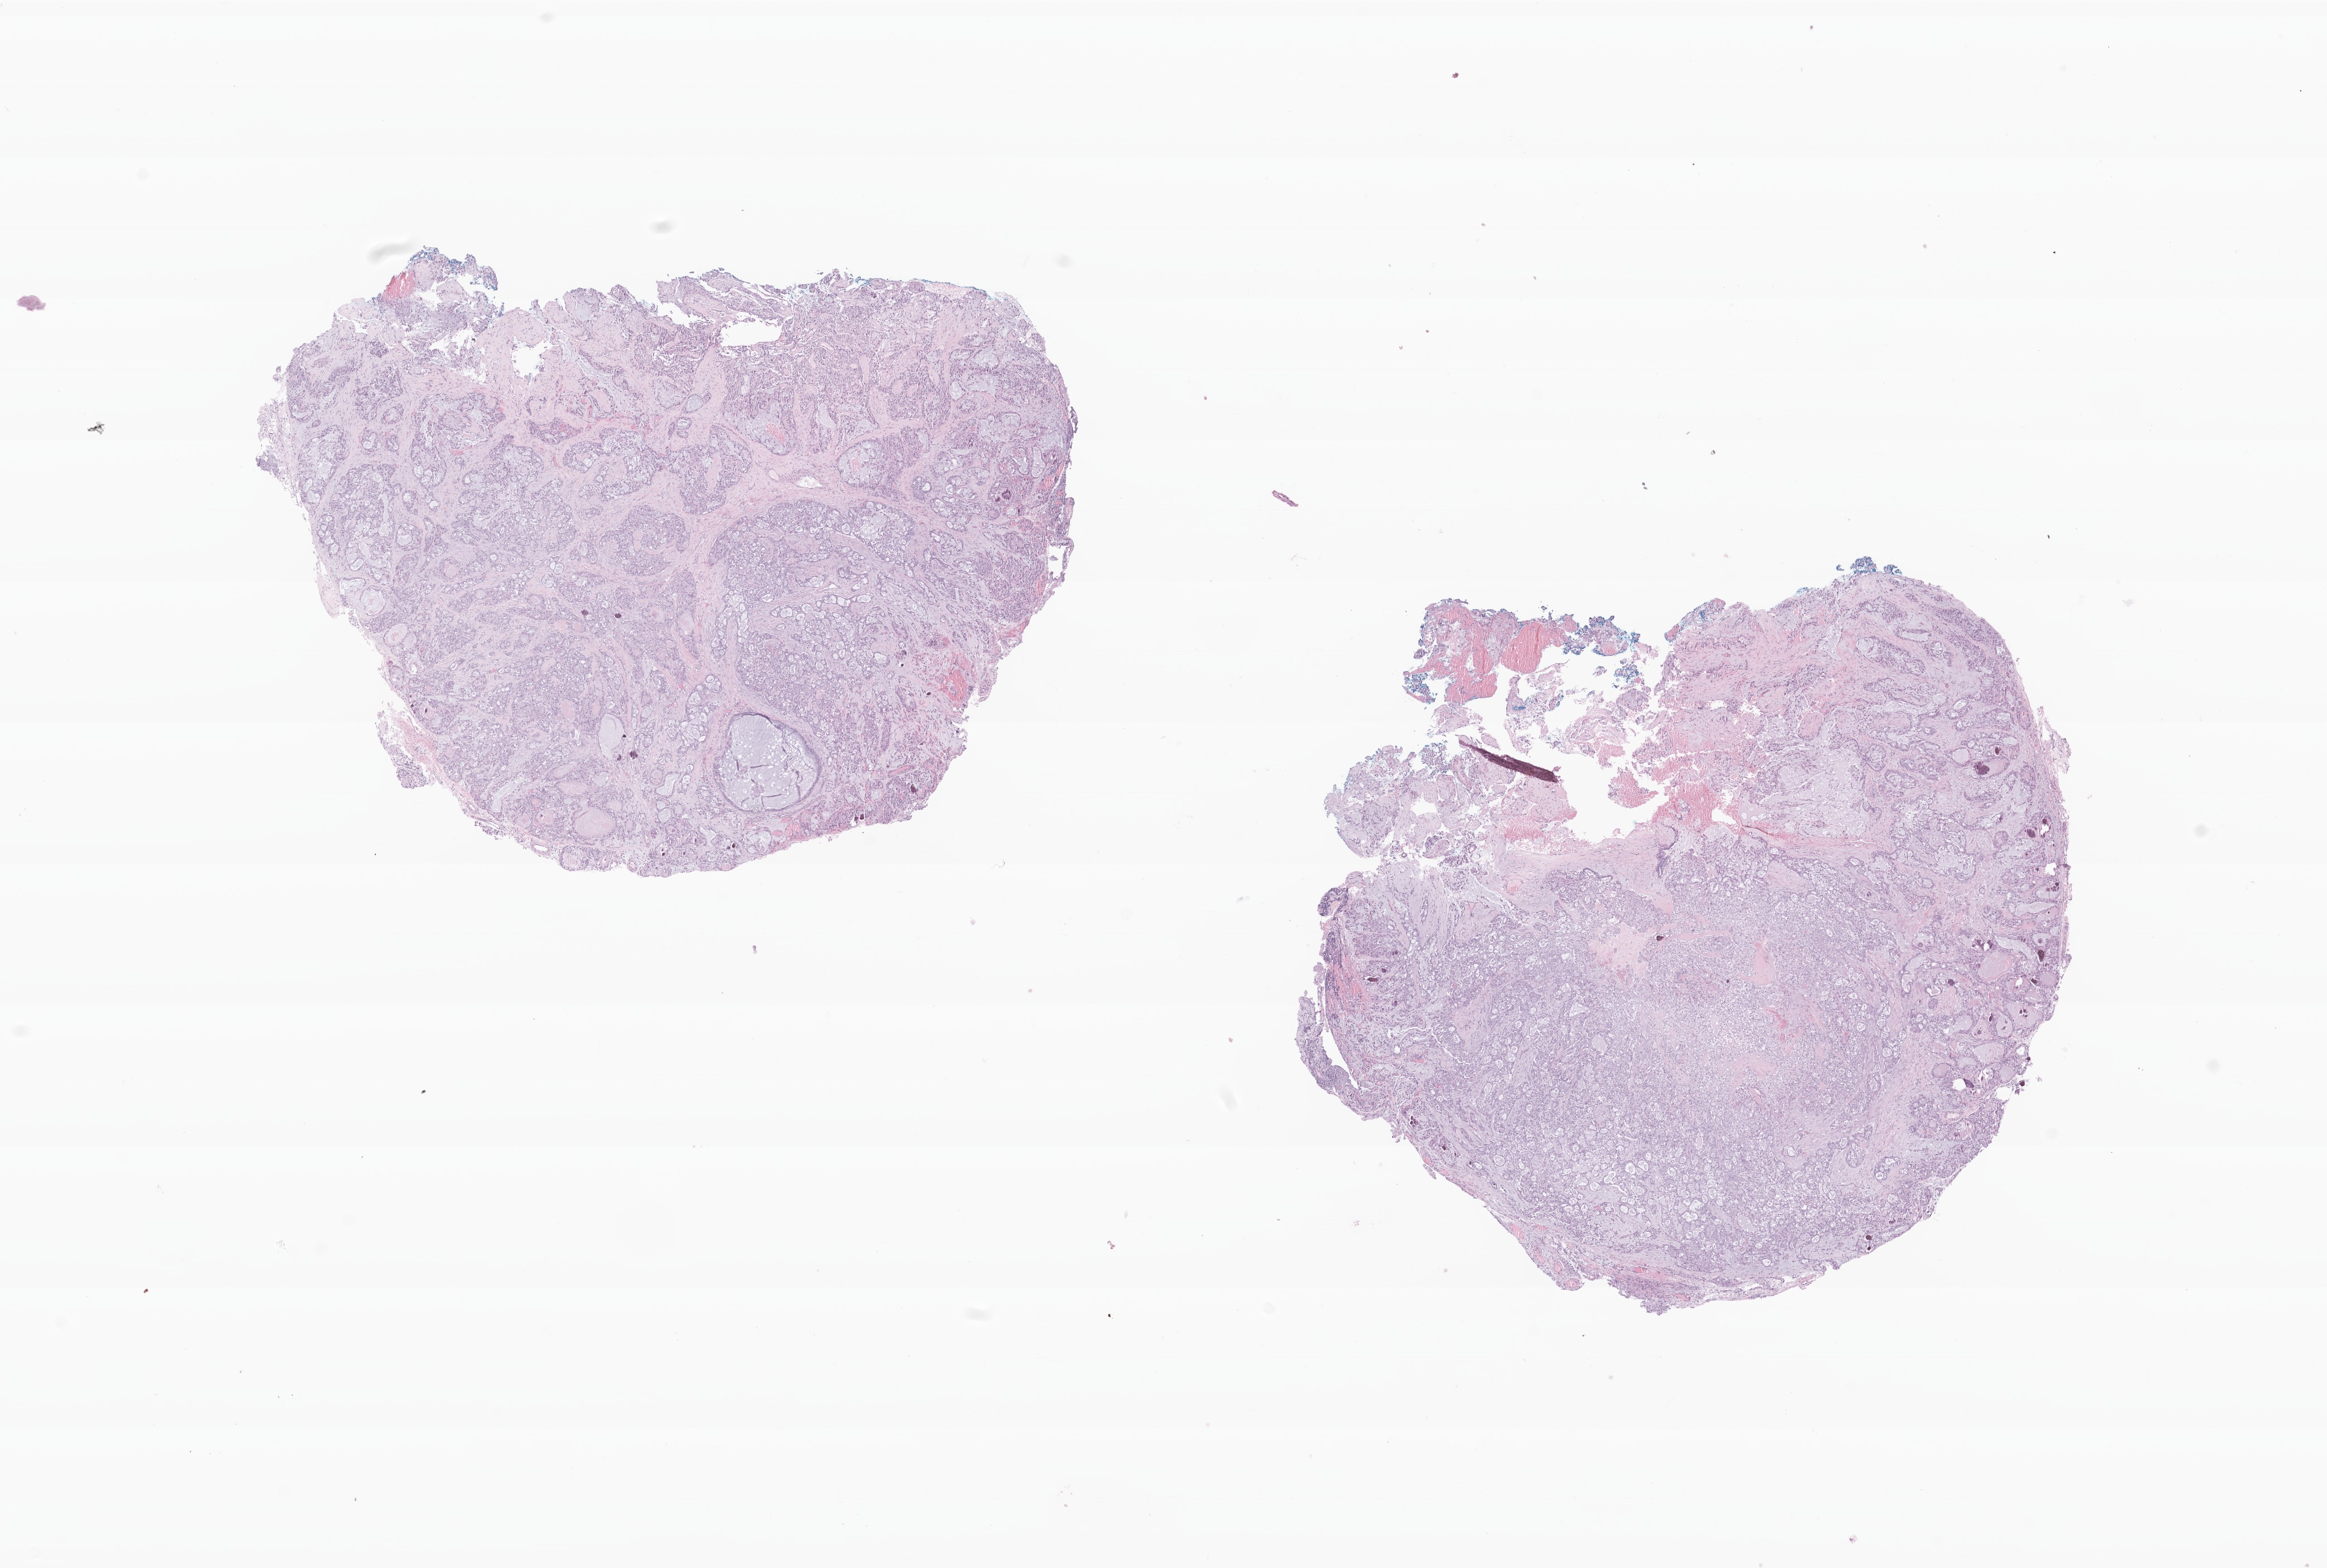
Hematoxylin and eosin (H&E) whole-slide image of tumor tissue from the lung — a low-resolution overview of the entire scanned area, about 17.5 x 11.8 mm. Formalin-fixed paraffin-embedded section. Patient male; age 210 months (17 years 6 months).
• diagnosis (ICD-O-3 morphology term): Mucoepidermoid carcinoma